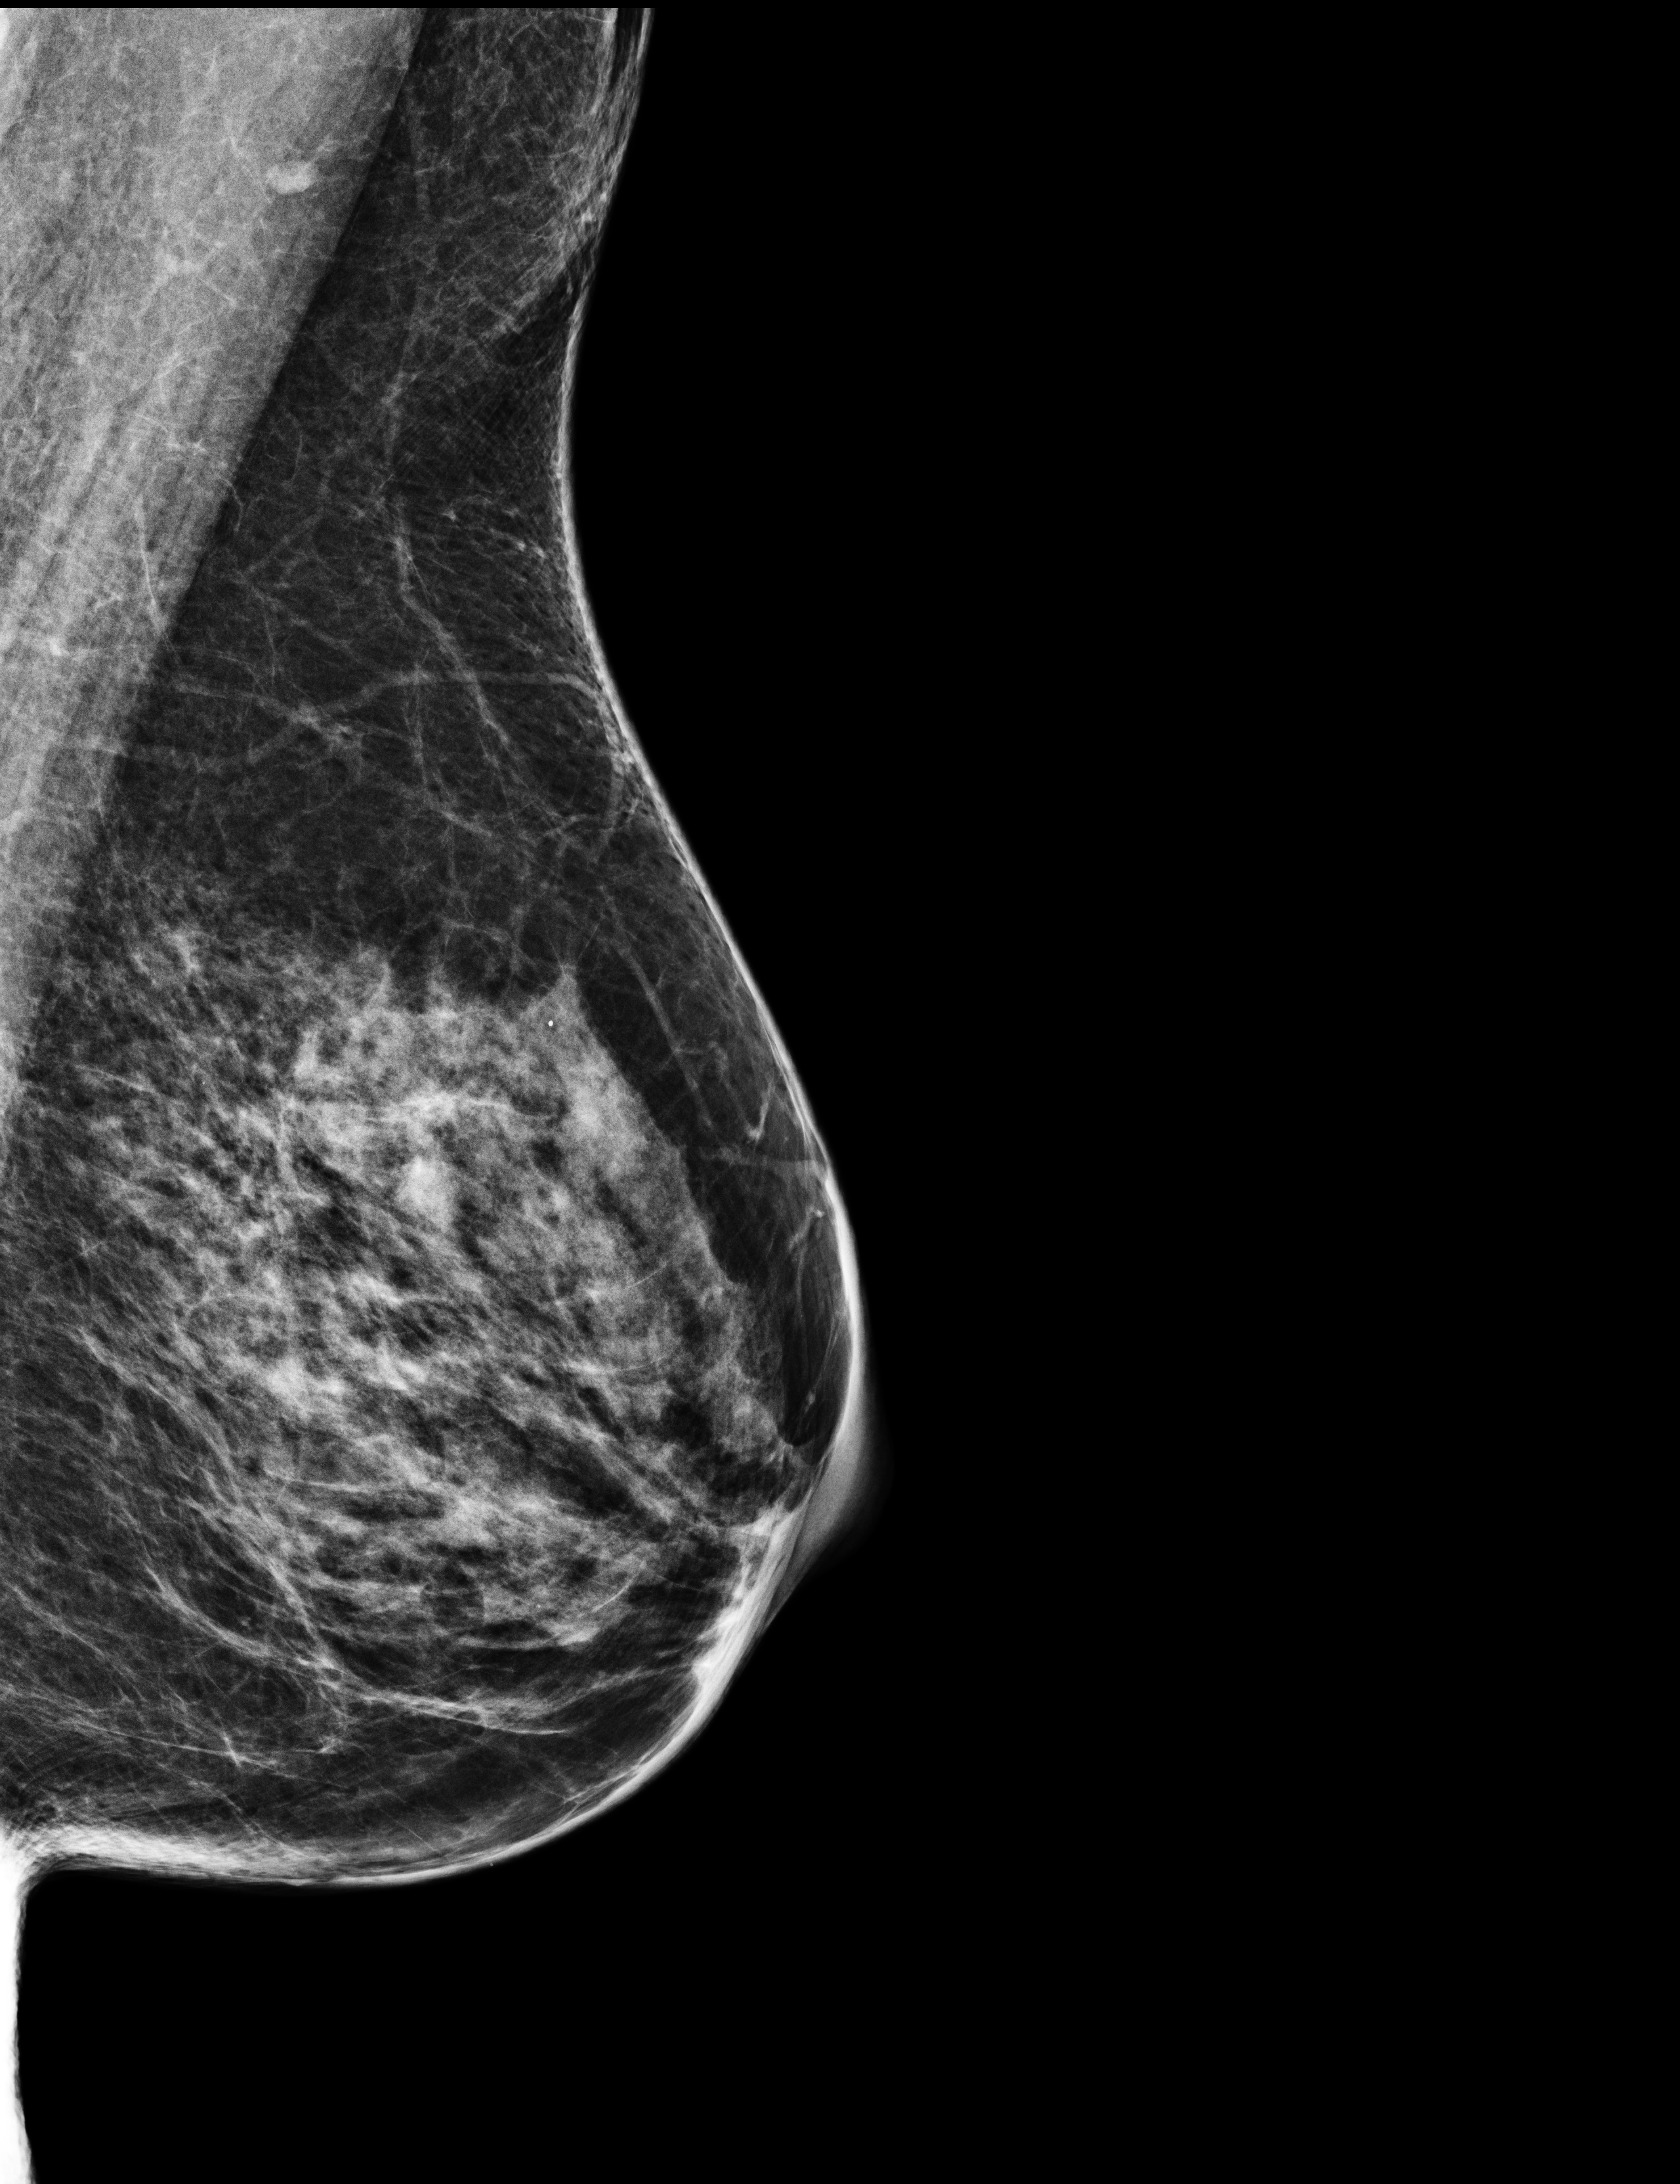
Digital mammogram (FFDM); left breast; medio-lateral oblique projection; annual screening mammography examination; compressed breast thickness 58 mm; system: Selenia Dimensions. Patient aged 60 years (female).
- BI-RADS breast density category at the screening exam (both breasts, scale 1–4): 3
- final BI-RADS assessment for this screening round (tomosynthesis exam, both breasts): category 1
- recall: no recall after this screen